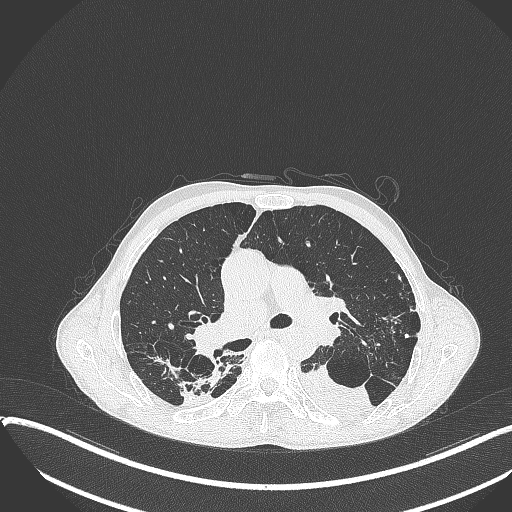
Chest CT, one axial slice; slice 236 of 401 in the series (ordered by position); 120 kVp; lung window (W 1500 / L -600 HU); 1 mm slice thickness; 512 × 512 image matrix, field of view 400 × 400 mm. Patient: male, 57 years. From the clinical record (not read from this slice): clinical TNM (as recorded): T4 N0 M0.
Structures marked on this image (bounding box drawn by a radiologist):
- lung tumour (recorded histology: squamous cell carcinoma): bounding box (x1, y1, x2, y2) in pixels: (298, 361, 375, 423)